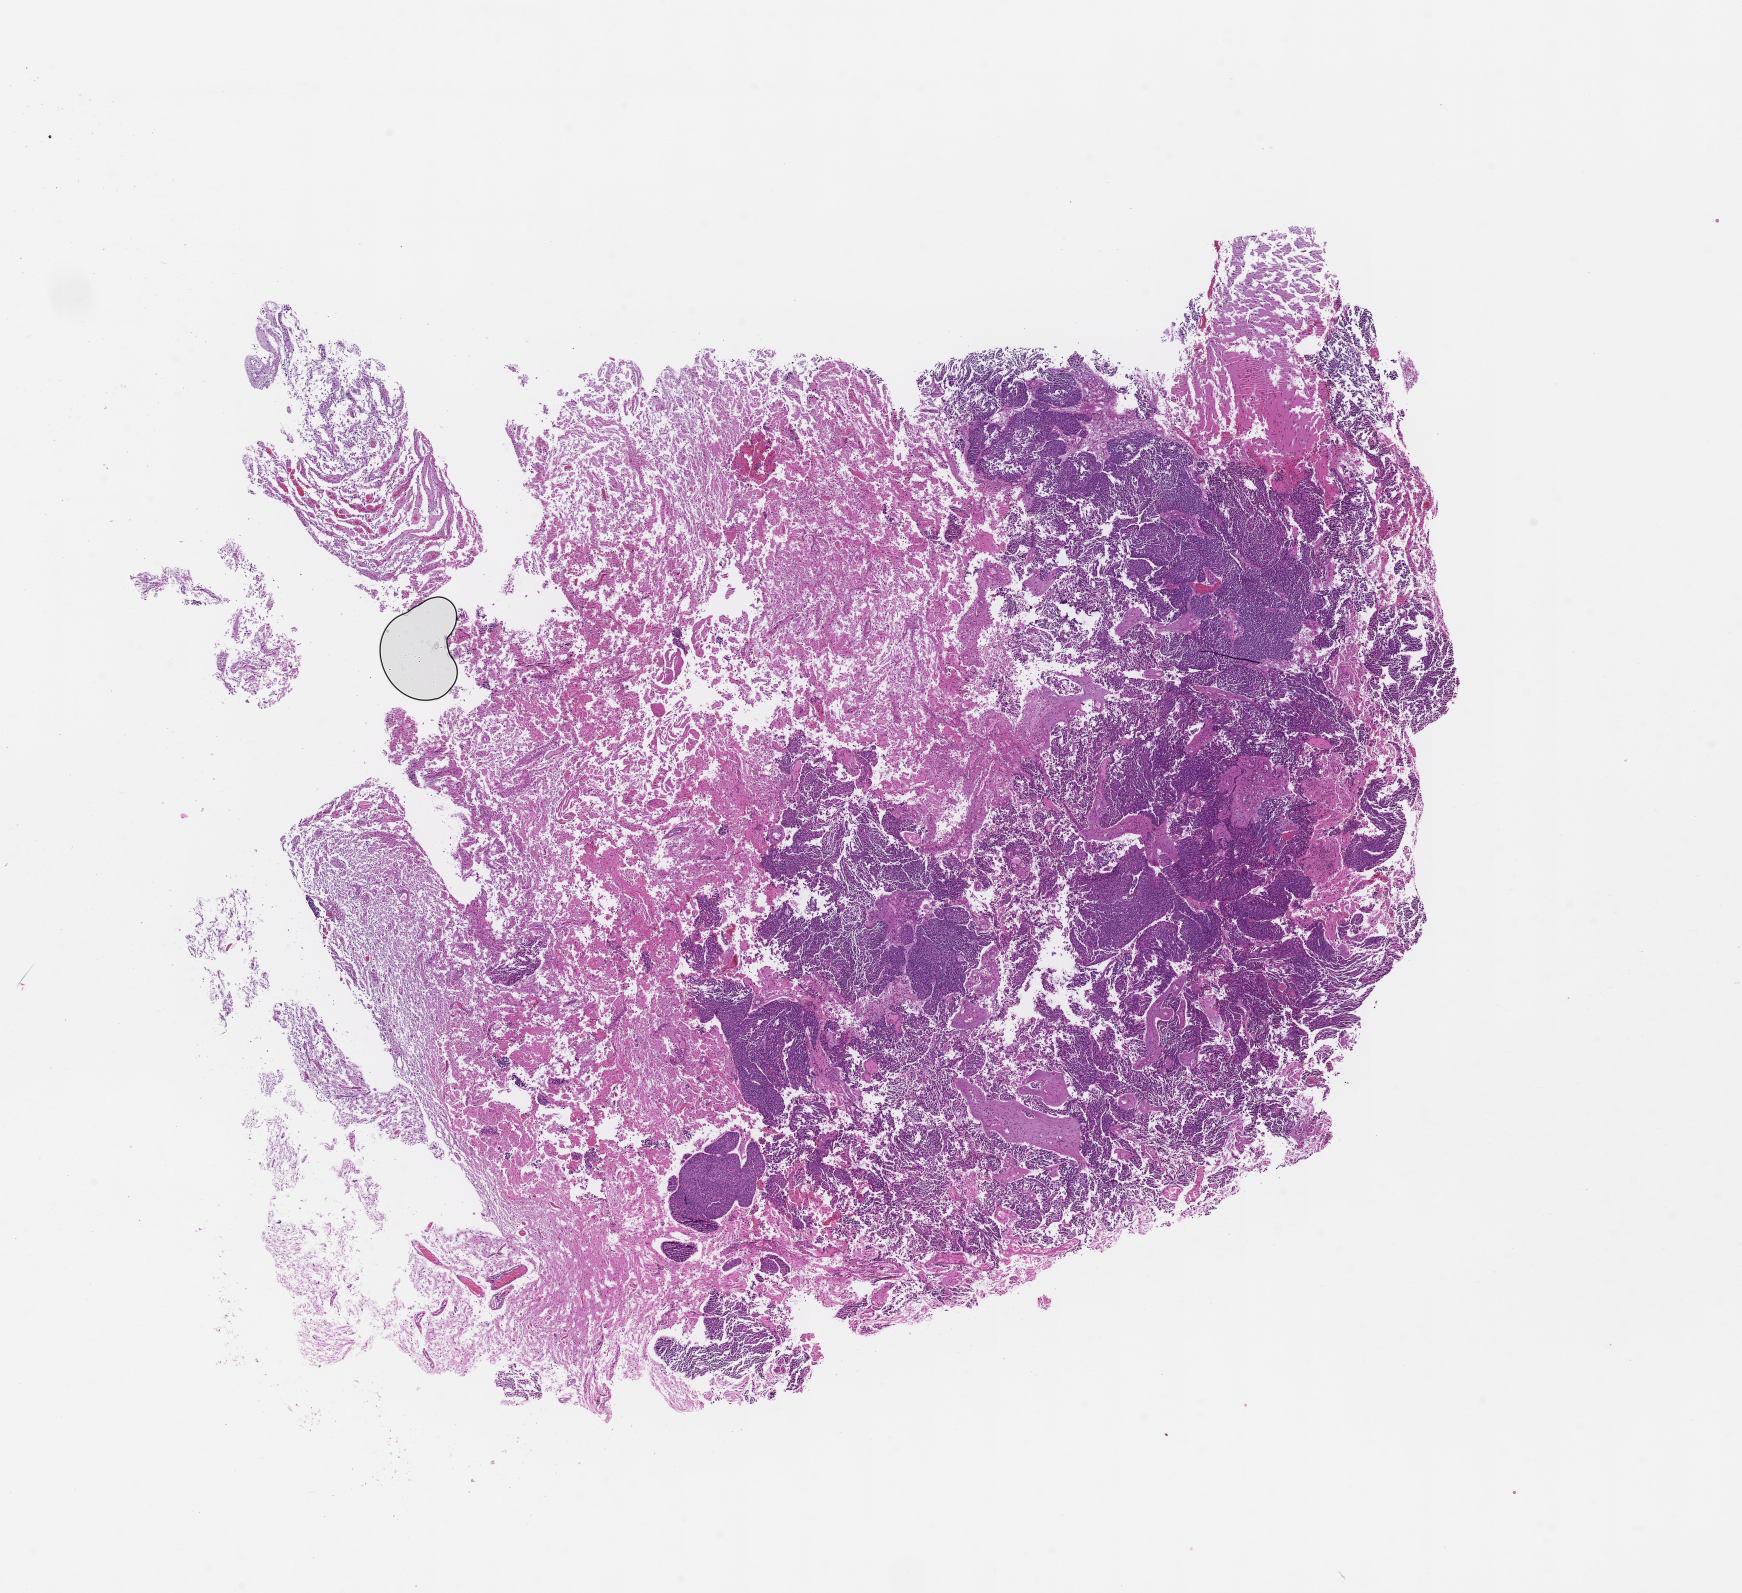
Digitized hematoxylin and eosin (H&E)-stained section — shown as a low-resolution overview of the whole scanned area (about 14.1 x 12.9 mm); FFPE section. Male patient.
This section: metastasis (sampled organ not recorded). Primary diagnosis of the patient: Non-Small Cell Lung Carcinoma.